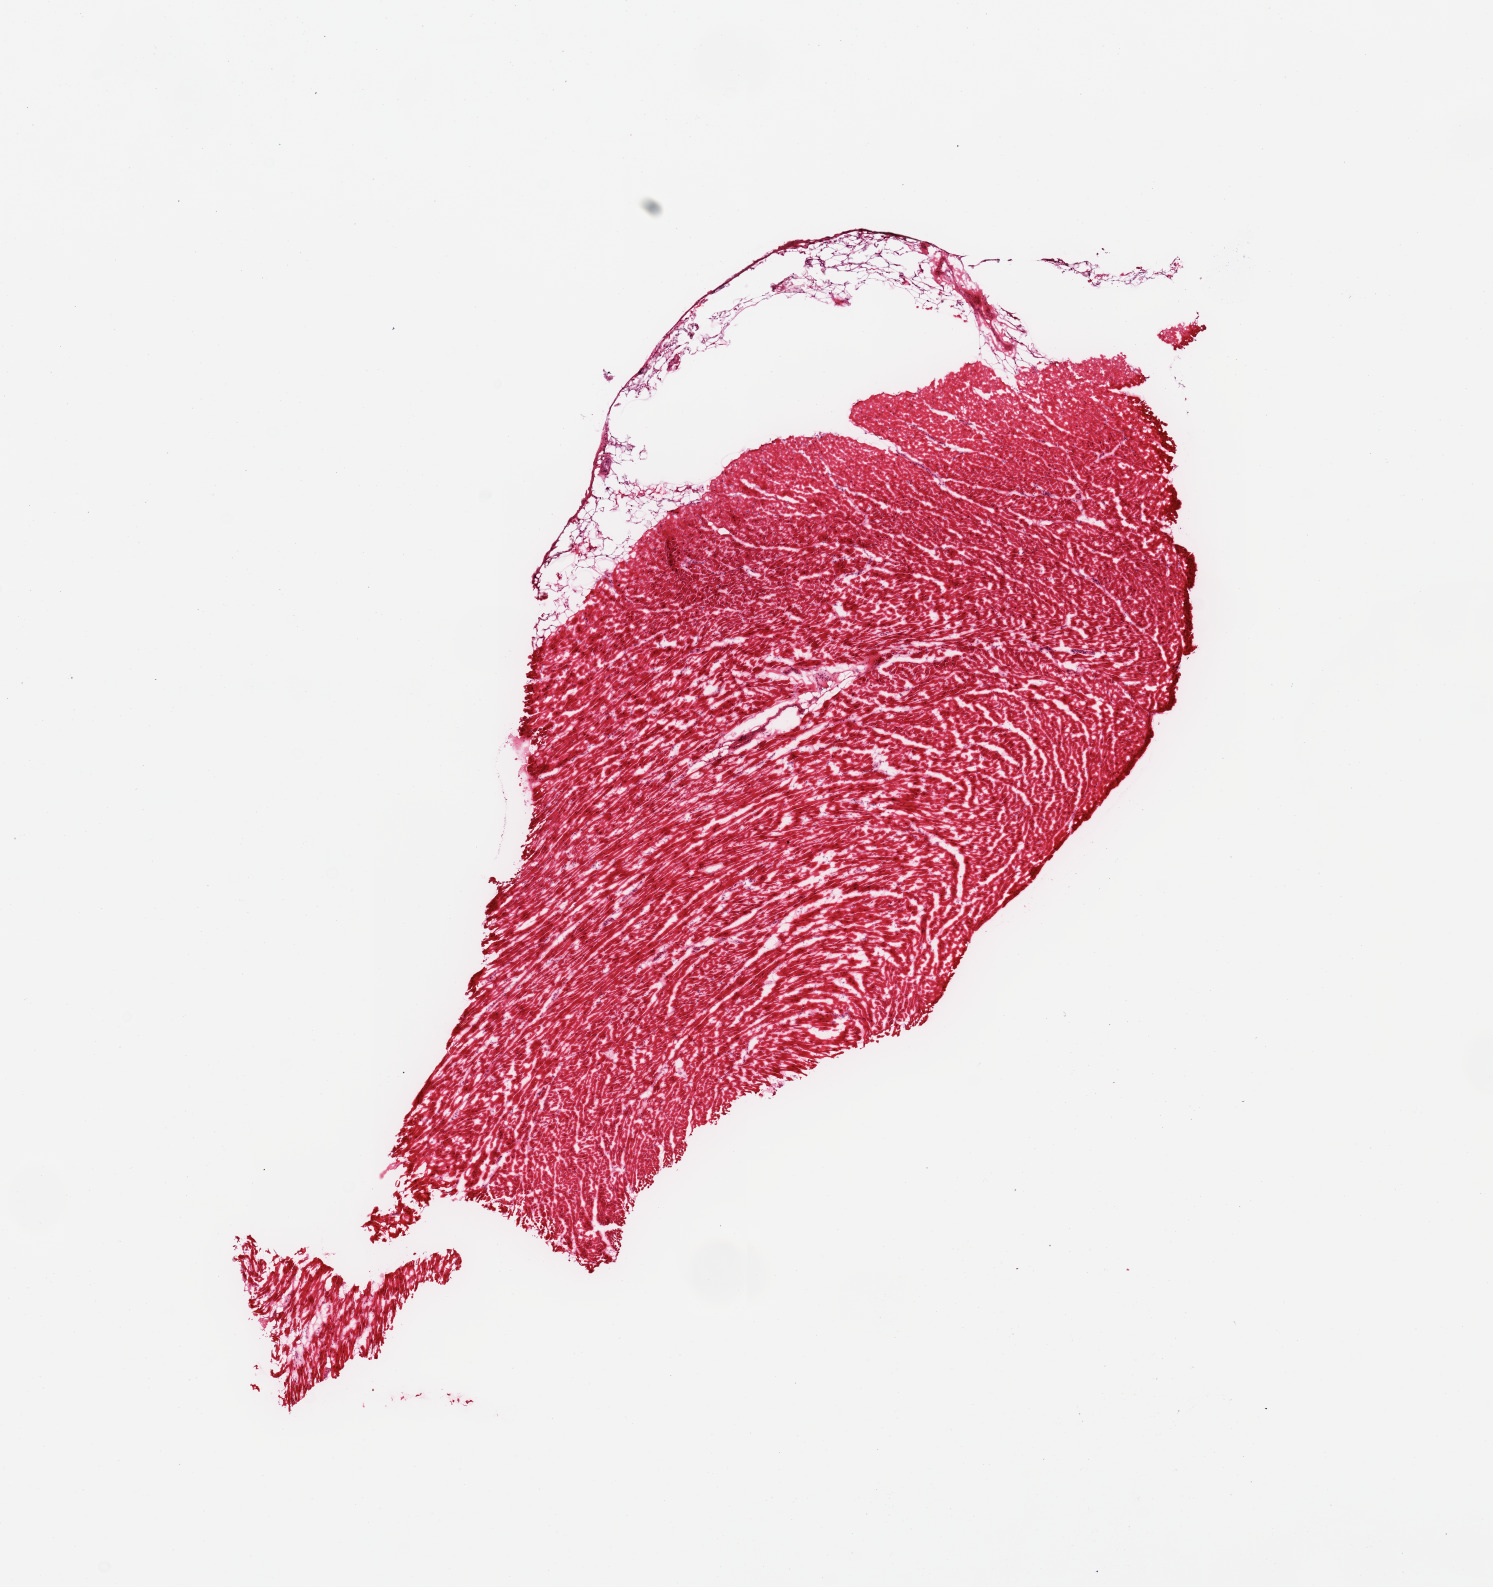
Digitized hematoxylin and eosin (H&E)-stained section, brightfield — low-resolution overview of the scanned area, about 11.8 x 12.6 mm (acquisition: 20x scan). Male donor.
- specimen: frozen section; section of heart (target tissue); tissue donor sample